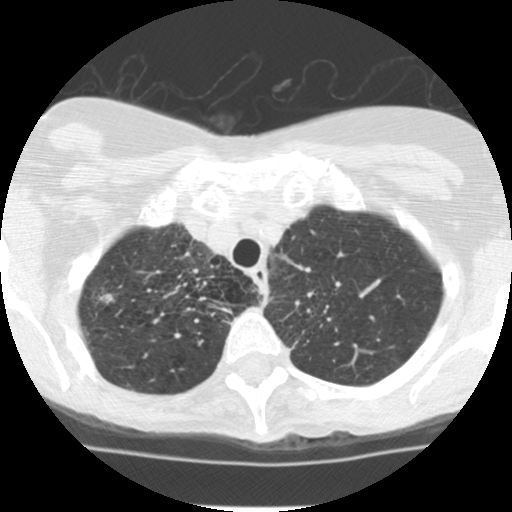
Chest CT (low-dose screening protocol), one axial image. First (baseline) screen. Lung window (W 1500 / L -600 HU). 2.5 mm slice thickness. Standard (soft-tissue) reconstruction kernel (STANDARD). Slice 26 of 135 in the series. Female participant, aged 68 years at enrolment. Current smoker at enrolment.
Expert reader's lesion annotation, bounding box [x1, y1, x2, y2] px = [66, 280, 127, 328]. The screening reader recorded 2 non-calcified nodules or masses ≥4 mm on this exam (right upper lobe, right upper lobe); which of them this box marks is not recorded. Later outcome: lung cancer diagnosed 411 days after this screen (after the second annual screen) — large cell neuroendocrine carcinoma, right upper lobe, undifferentiated (G4), stage IB (AJCC 6th edition), 22 mm at pathology.